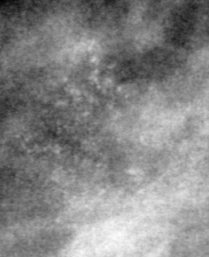
Cropped region of a digitized screen-film mammogram centred on a radiologist-marked abnormality; left breast; MLO view.
Finding: calcifications, morphology pleomorphic, distribution clustered; BI-RADS assessment category 4; subtlety rating 2 on a 1 (subtle) to 5 (obvious) scale; pathology result (as recorded, not read from the image): malignant.